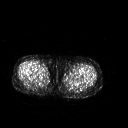
FDG PET of an extremity soft-tissue mass (from a PET/CT study), one axial slice. Slice 220 of 267 in the series (ordered by position). 3.27 mm slice thickness. 128 × 128 image matrix. Patient: female, 42 years. From the clinical record (not read from this slice): histological type: pleiomorphic leiomyosarcoma; grade: intermediate; site of the primary tumour: left thigh.
Outlined on this slice (expert contour drawn on MRI and transferred to this co-registered scan by the dataset authors):
- gross tumour volume including surrounding oedema: bounding box (x1, y1, x2, y2) in pixels: (66, 74, 81, 80)